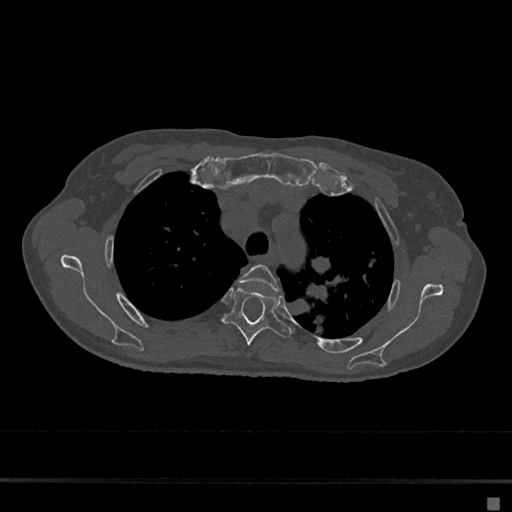
CT including the spine, one axial slice; slice 509 of 797 in the series (ordered by position); reconstruction kernel Br40s/3; 120 kVp; bone window (W 1800 / L 400 HU); 0.5 mm slice thickness; 512 × 512 image matrix. Patient: female, 68 years. Case-level facts recorded for this patient, not image findings: primary cancer: renal.
Annotated regions visible in this slice (semi-automatic segmentation, software-assisted and operator-edited):
- T3 vertebra: bounding box (x1, y1, x2, y2) in pixels: (239, 264, 279, 292)
- T4 vertebra: (223, 287, 292, 345)